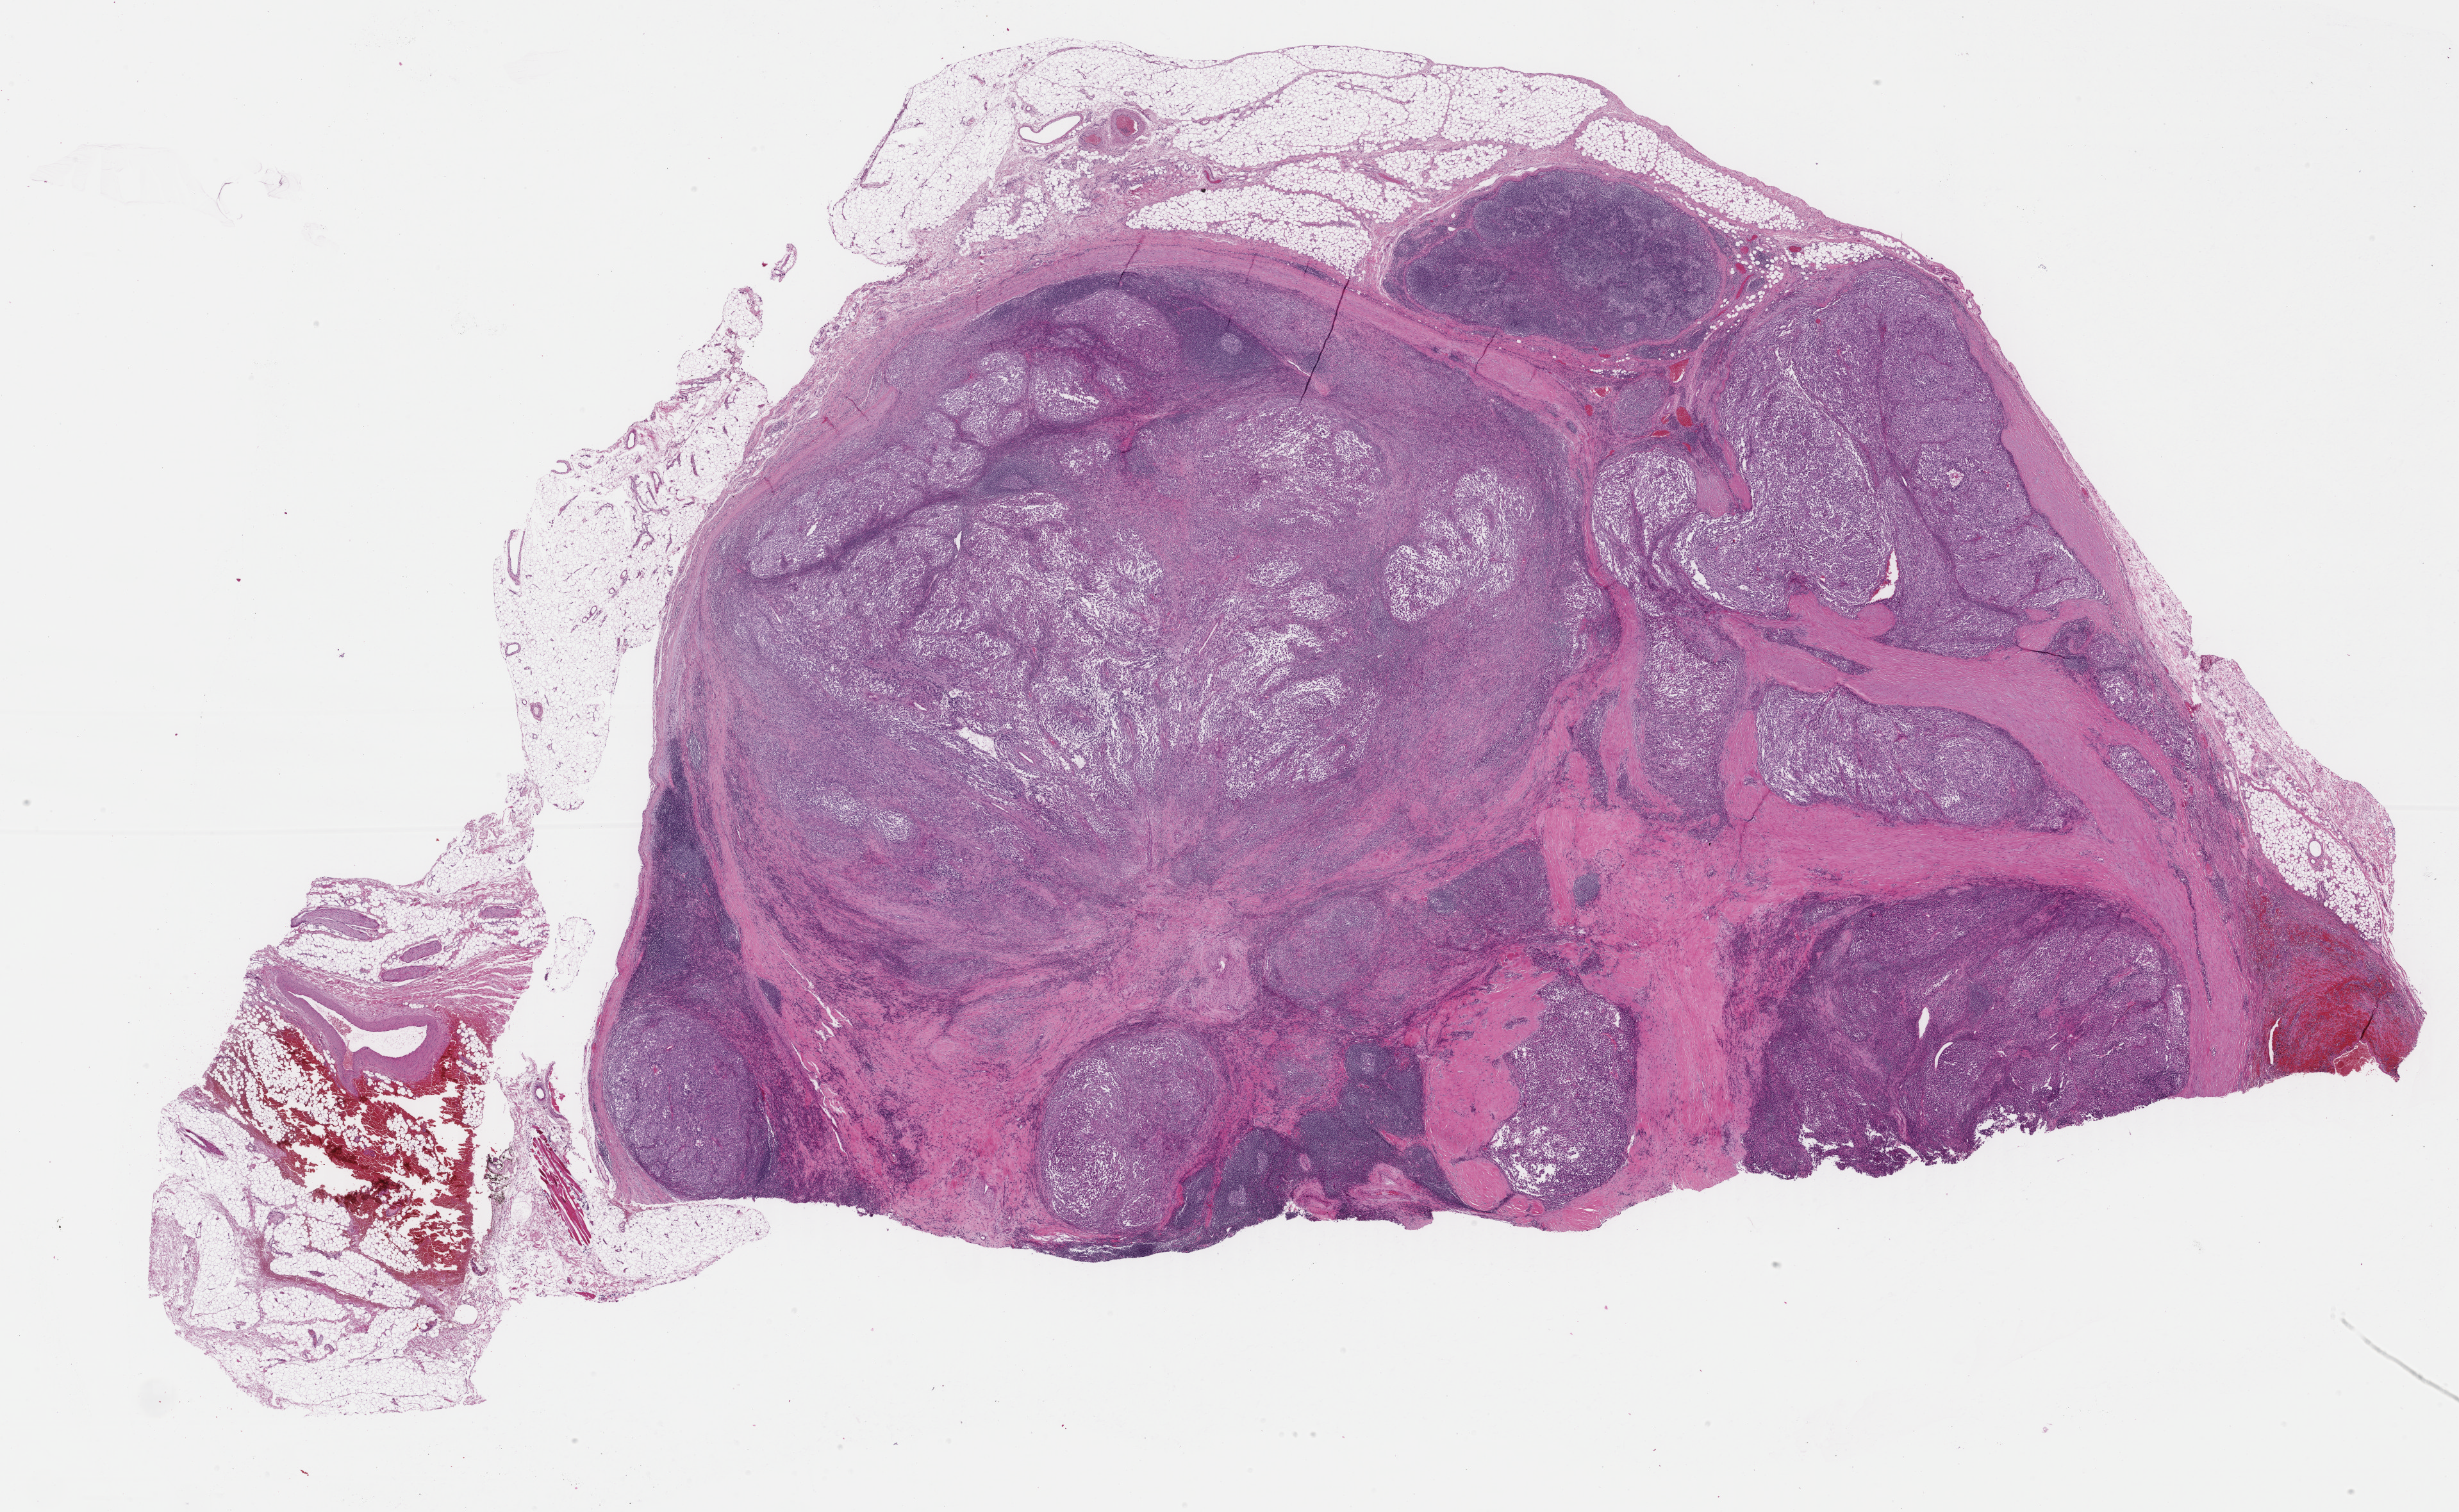
Whole-slide histology image, H&E — a low-resolution overview of the entire scanned area, about 30.5 x 18.7 mm. Formalin-fixed paraffin-embedded (FFPE) diagnostic section. Primary tumour sample from the skin. Male, age 44 years at initial diagnosis.
• pathologic diagnosis: Amelanotic melanoma